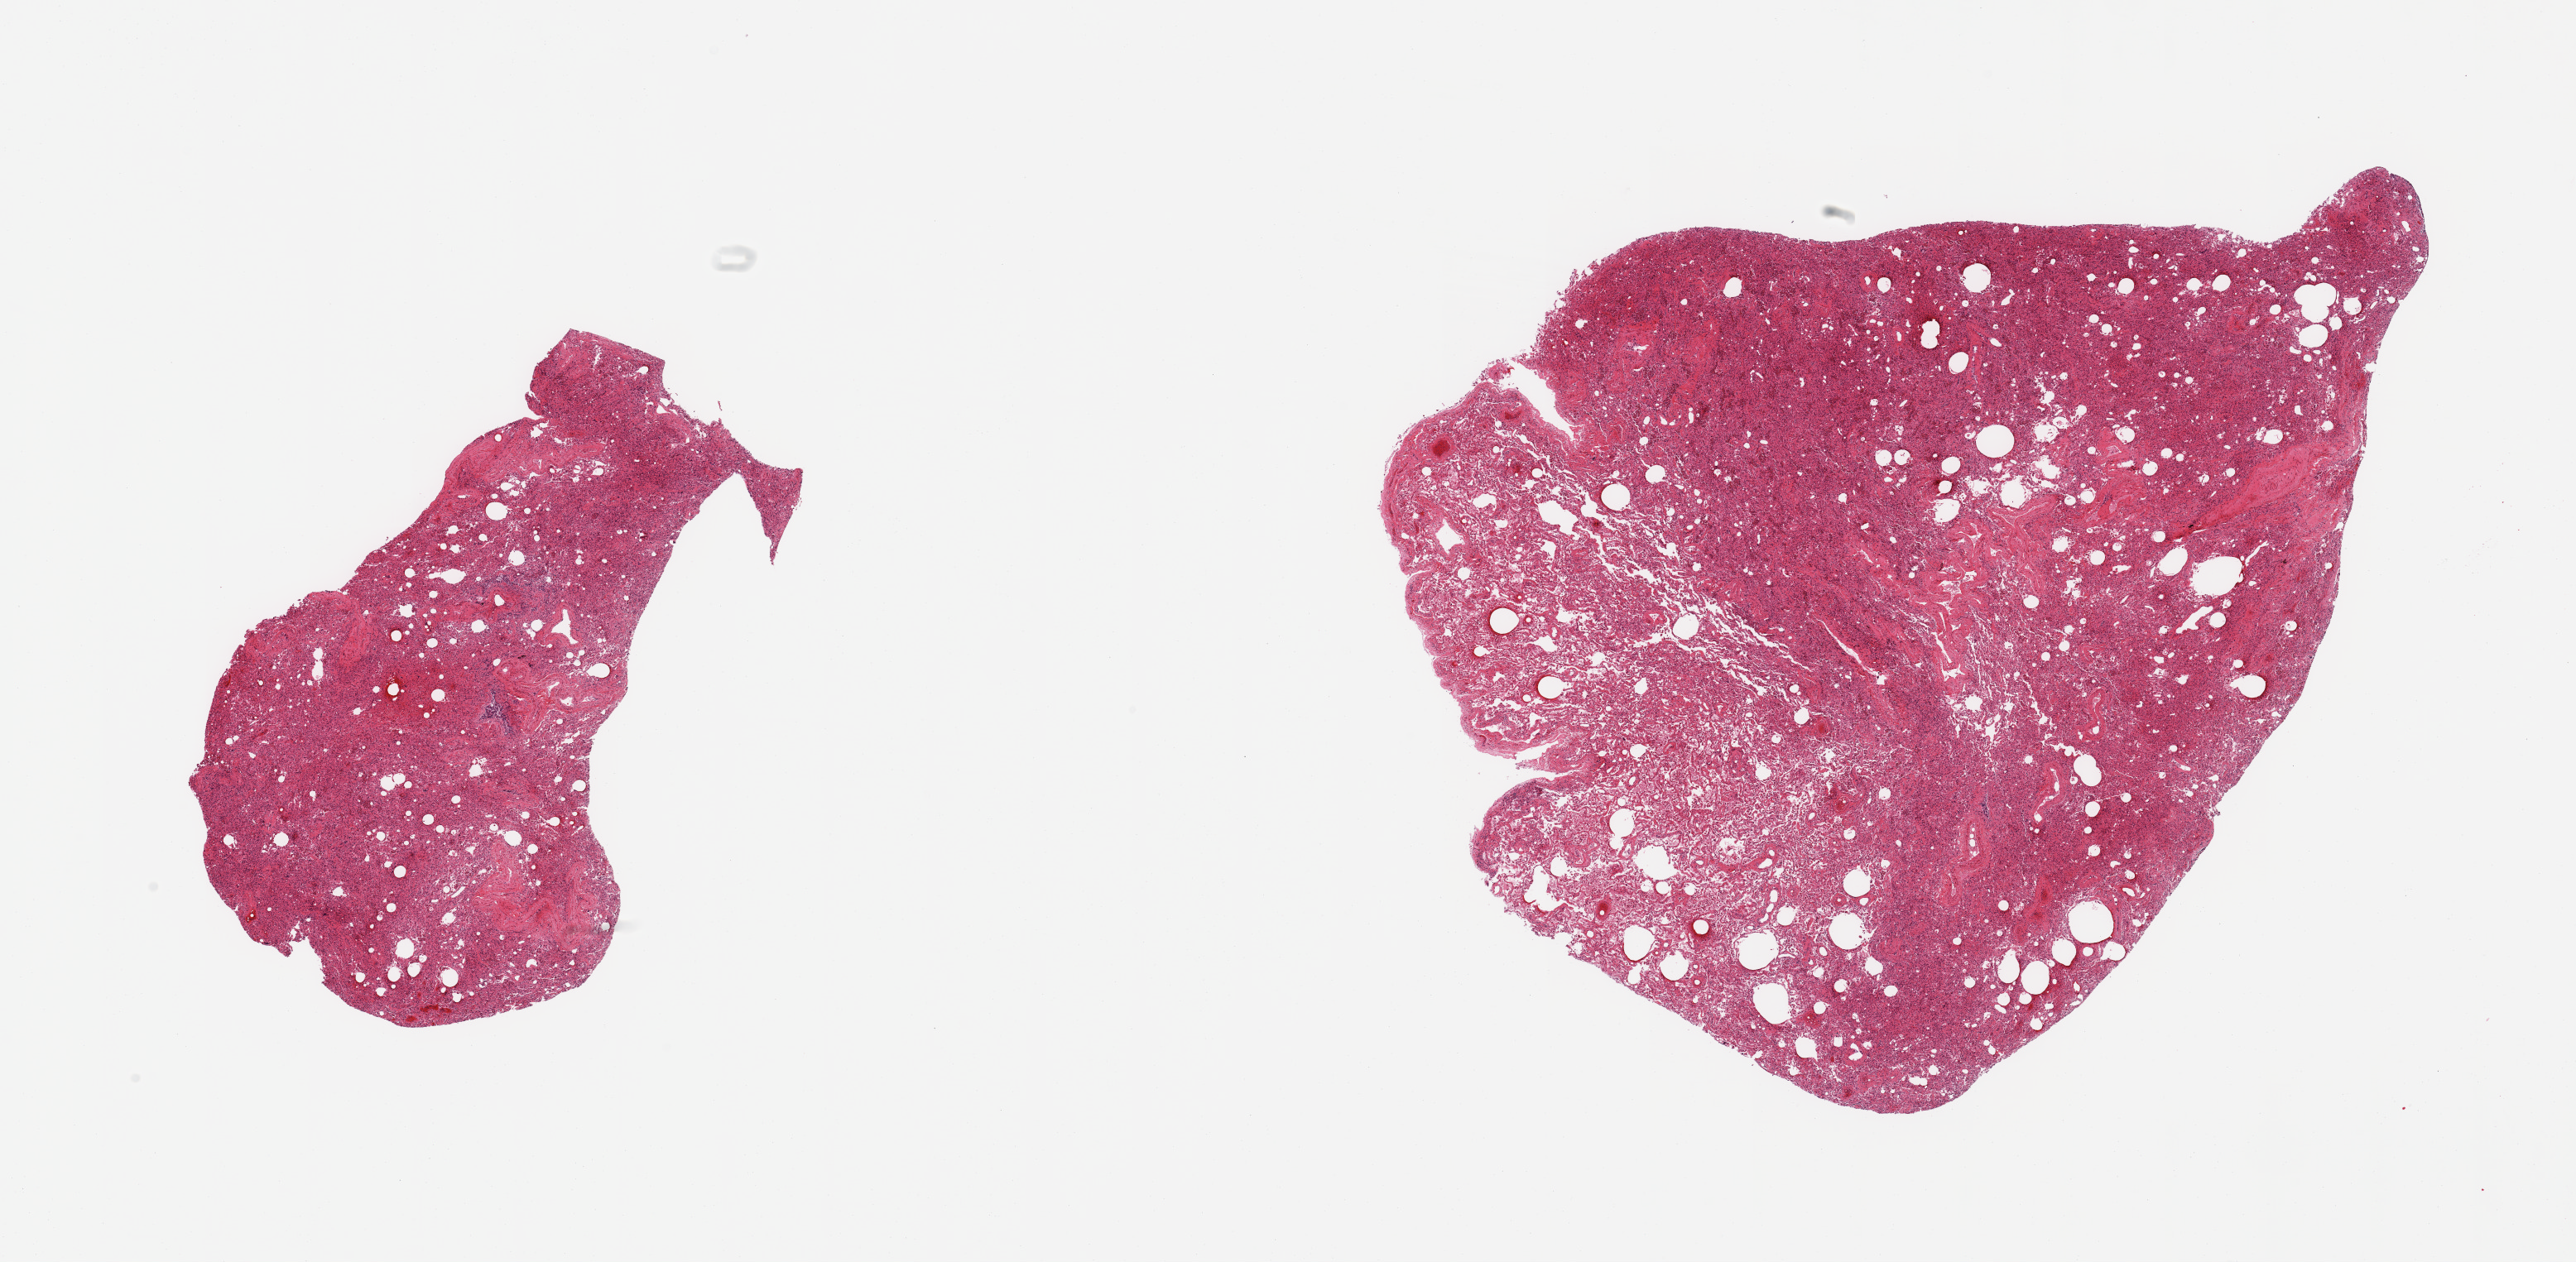
Digitized H&E-stained section — whole scanned area (about 24.6 x 12.1 mm) shown as a low-resolution overview, PAXgene-fixed, paraffin-embedded tissue, sampled site (target tissue): lung, donor tissue sample.
Reviewer comment on this tissue sample: 2 pieces; collapse, some fibrosis, pulmonary macrophages, some congestion, sloughed bronchial epithelium.